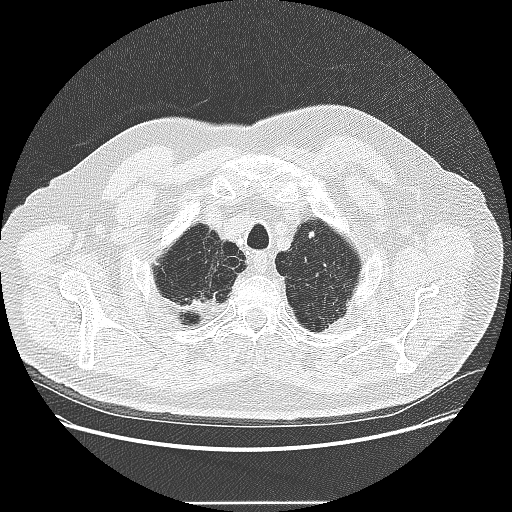
Low-dose screening chest CT, one axial slice. Lung window (W 1500 / L -600 HU). 2.5 mm slice thickness. 512 × 512 image matrix, field of view 400 × 400 mm.
Structures marked on this image (expert manual segmentation):
- lesion 1 (tumor, upper lobe of left lung): bounding box (x1, y1, x2, y2) in pixels: (308, 230, 315, 242)